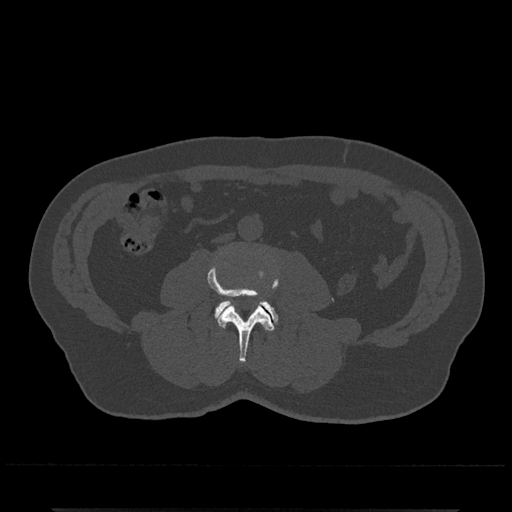
CT including the spine, one axial slice; slice 202 of 797 in the series (ordered by position); 120 kVp; bone window (W 1800 / L 400 HU); 0.5 mm slice thickness; 512 × 512 image matrix, field of view 393 × 393 mm. Male patient, age 67 years. Case-level facts recorded for this patient, not image findings: primary cancer: prostate.
Outlined on this slice (semi-automatic segmentation, software-assisted and operator-edited):
- L3 vertebra: bounding box [x1, y1, x2, y2] px = [208, 262, 279, 362]
- L4 vertebra: [214, 300, 279, 326]